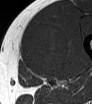
MRI of an extremity soft-tissue mass, one axial slice. Slice 32 of 62 in the series (ordered by position). MR volume resampled by the dataset authors to the PET/CT grid (not the native acquisition matrix). 92 × 104 image matrix, field of view 90 × 102 mm. Male patient. Case-level facts recorded for this patient, not image findings: histological type: mixoid liposarcoma; grade: low; site of the primary tumour: left thigh.
Outlined on this slice (expert contour drawn on MRI and transferred to this co-registered scan by the dataset authors):
- gross tumour volume (mass): box from (x=21, y=22) to (x=70, y=77) px